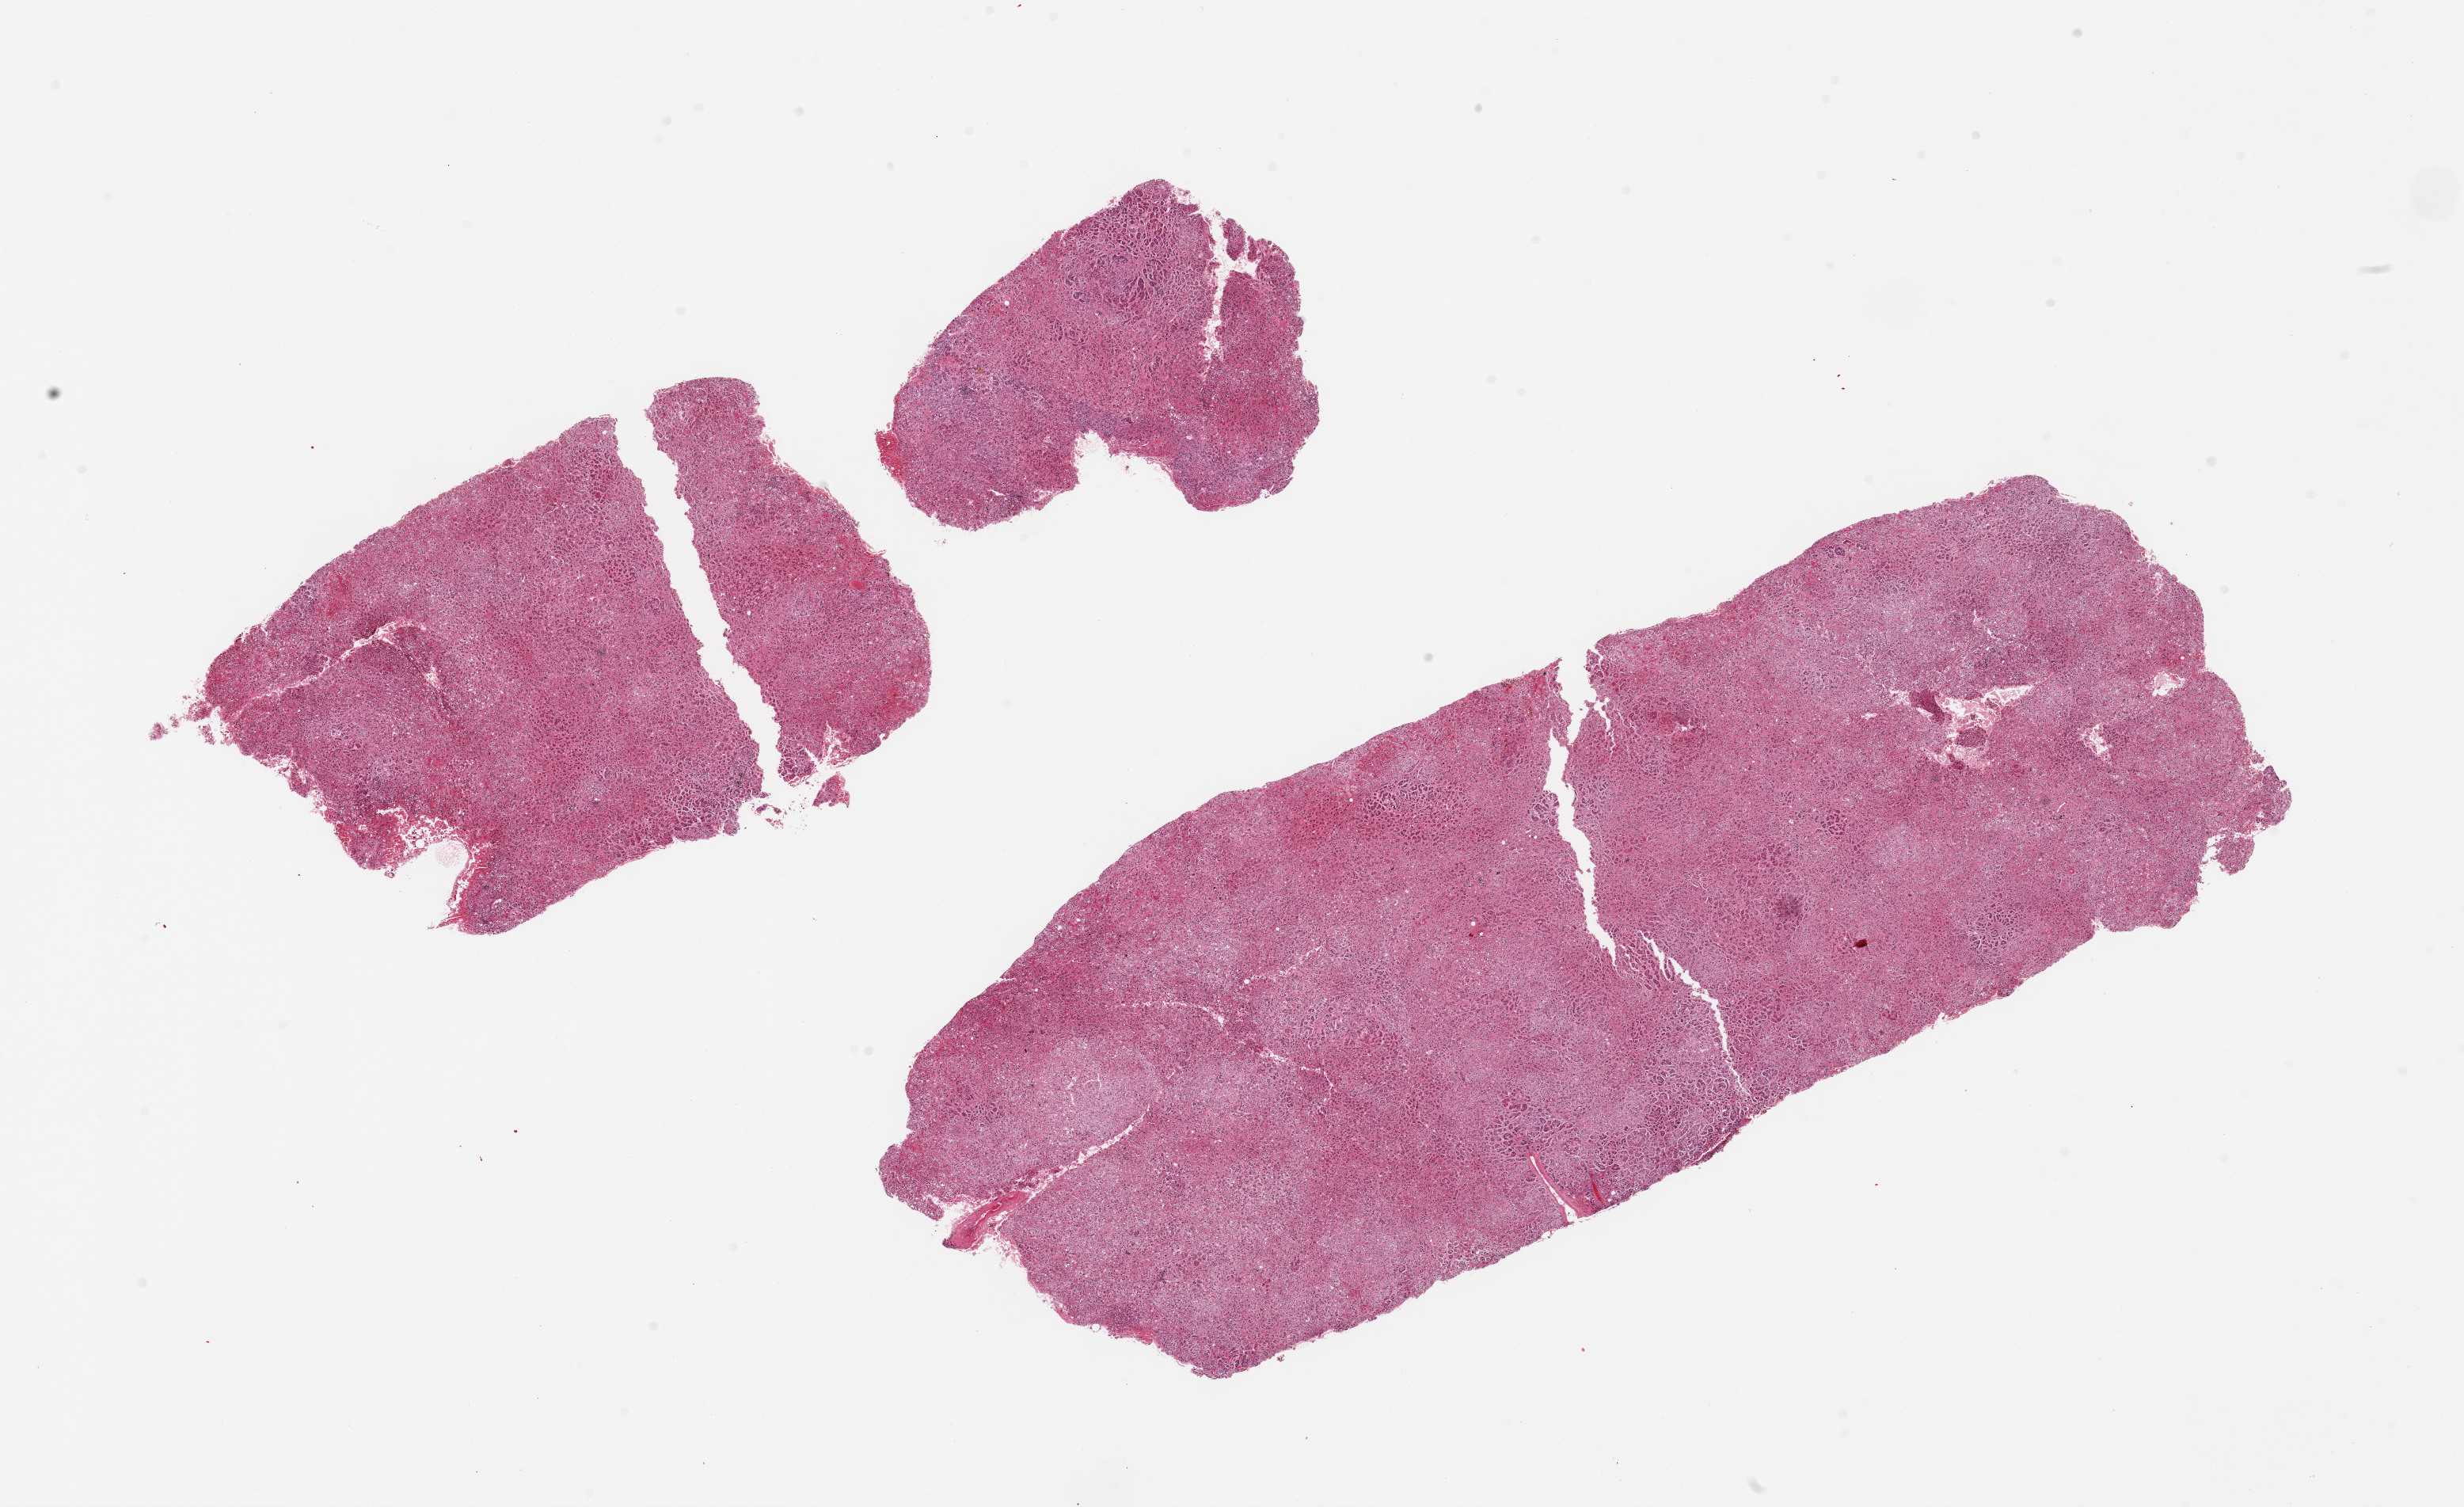
H&E whole-slide image — whole scanned area (about 24.6 x 15.0 mm, slide scanned at 20x) shown as a low-resolution overview, PAXgene-fixed paraffin-embedded (PFPE) section, target tissue: adrenal gland, donor tissue sample. Donor sex: male.
Review note (as recorded): 2 pieces, all cortex, minimal fat.